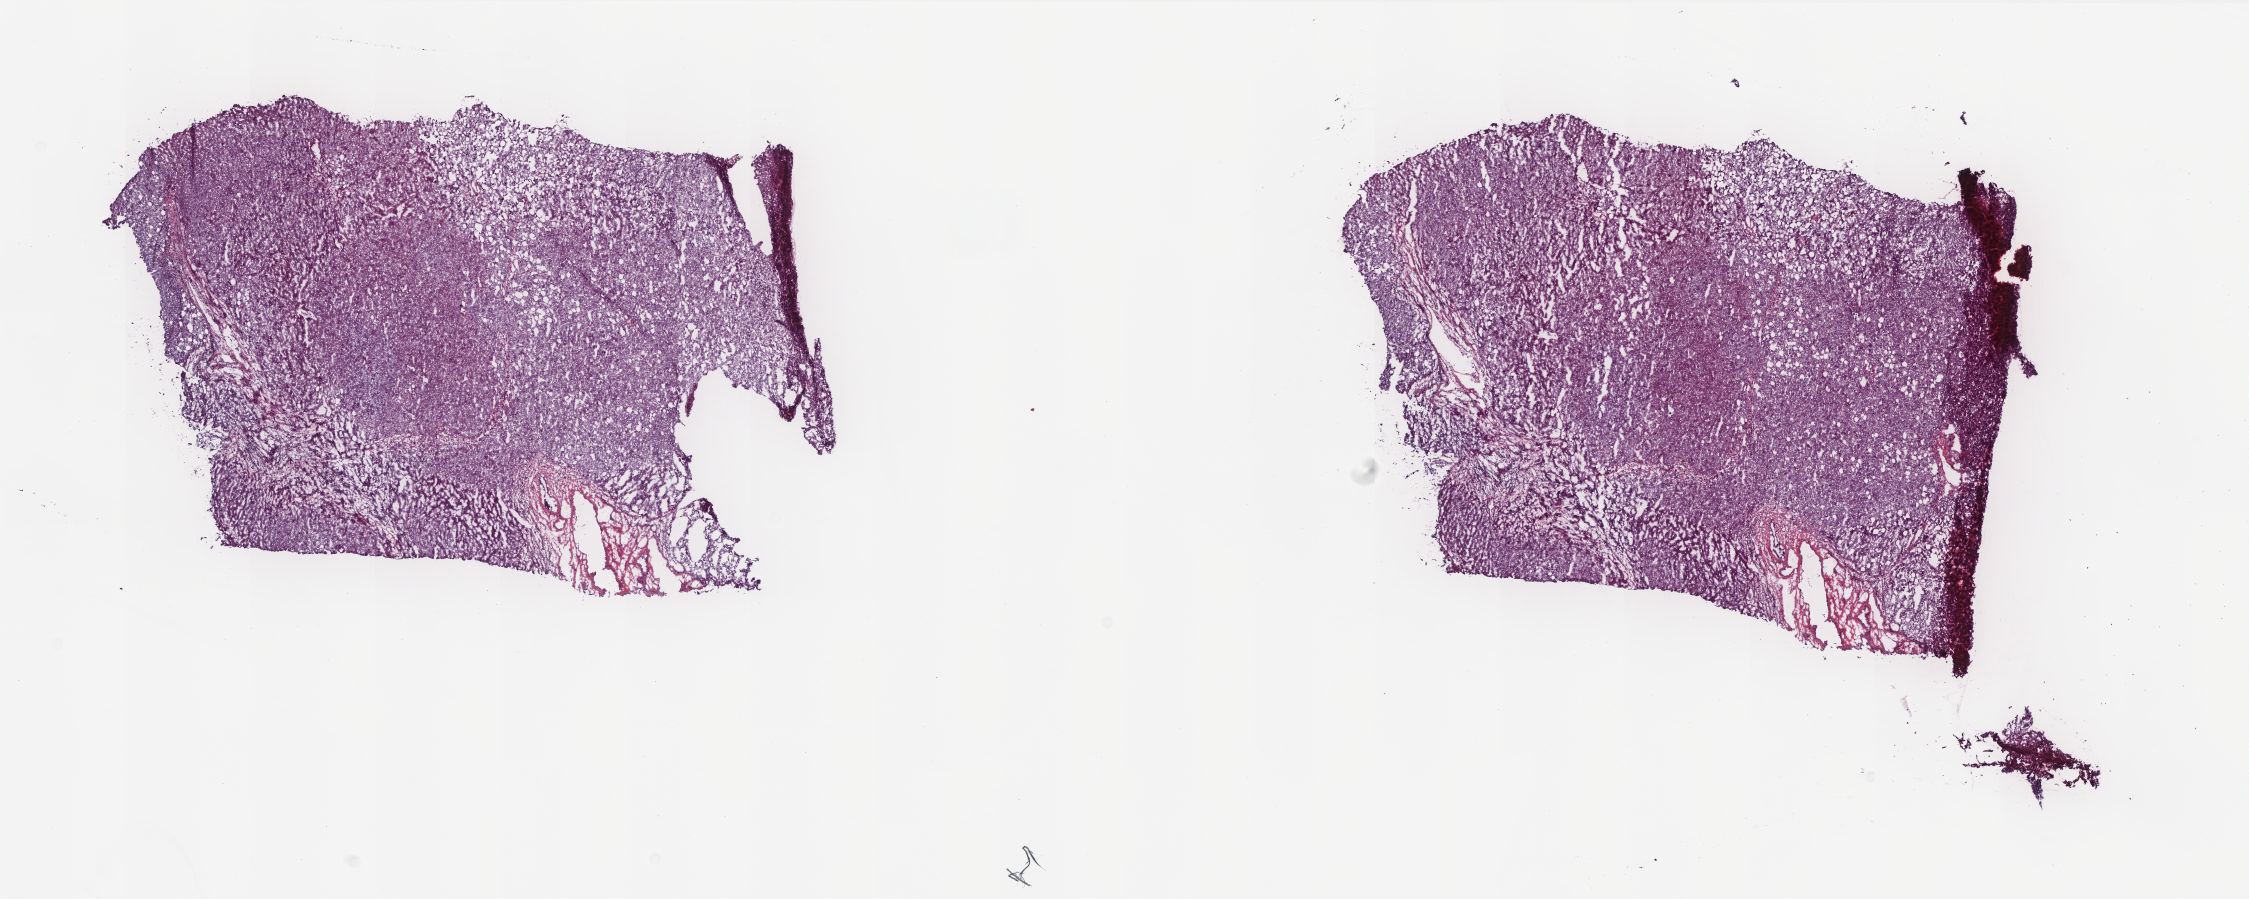
H&E-stained whole-slide image — a low-resolution overview of the entire scanned area, about 18.0 x 7.2 mm, frozen section from the top of the tissue portion, solid tissue normal (non-tumour tissue) sample from the liver. Male patient; age at initial diagnosis 62 years. Pathologist review of this section (percent, as recorded): tumour cells 0%, tumour nuclei 0%, normal cells 100%, stromal cells 0%, necrosis 0%. Infiltration values recorded for this section: lymphocyte infiltration 0%, monocyte infiltration 0%, neutrophil infiltration 0%.
This section: solid tissue normal (non-tumour) sample from the same patient. Patient diagnosis: Hepatocellular carcinoma, NOS.